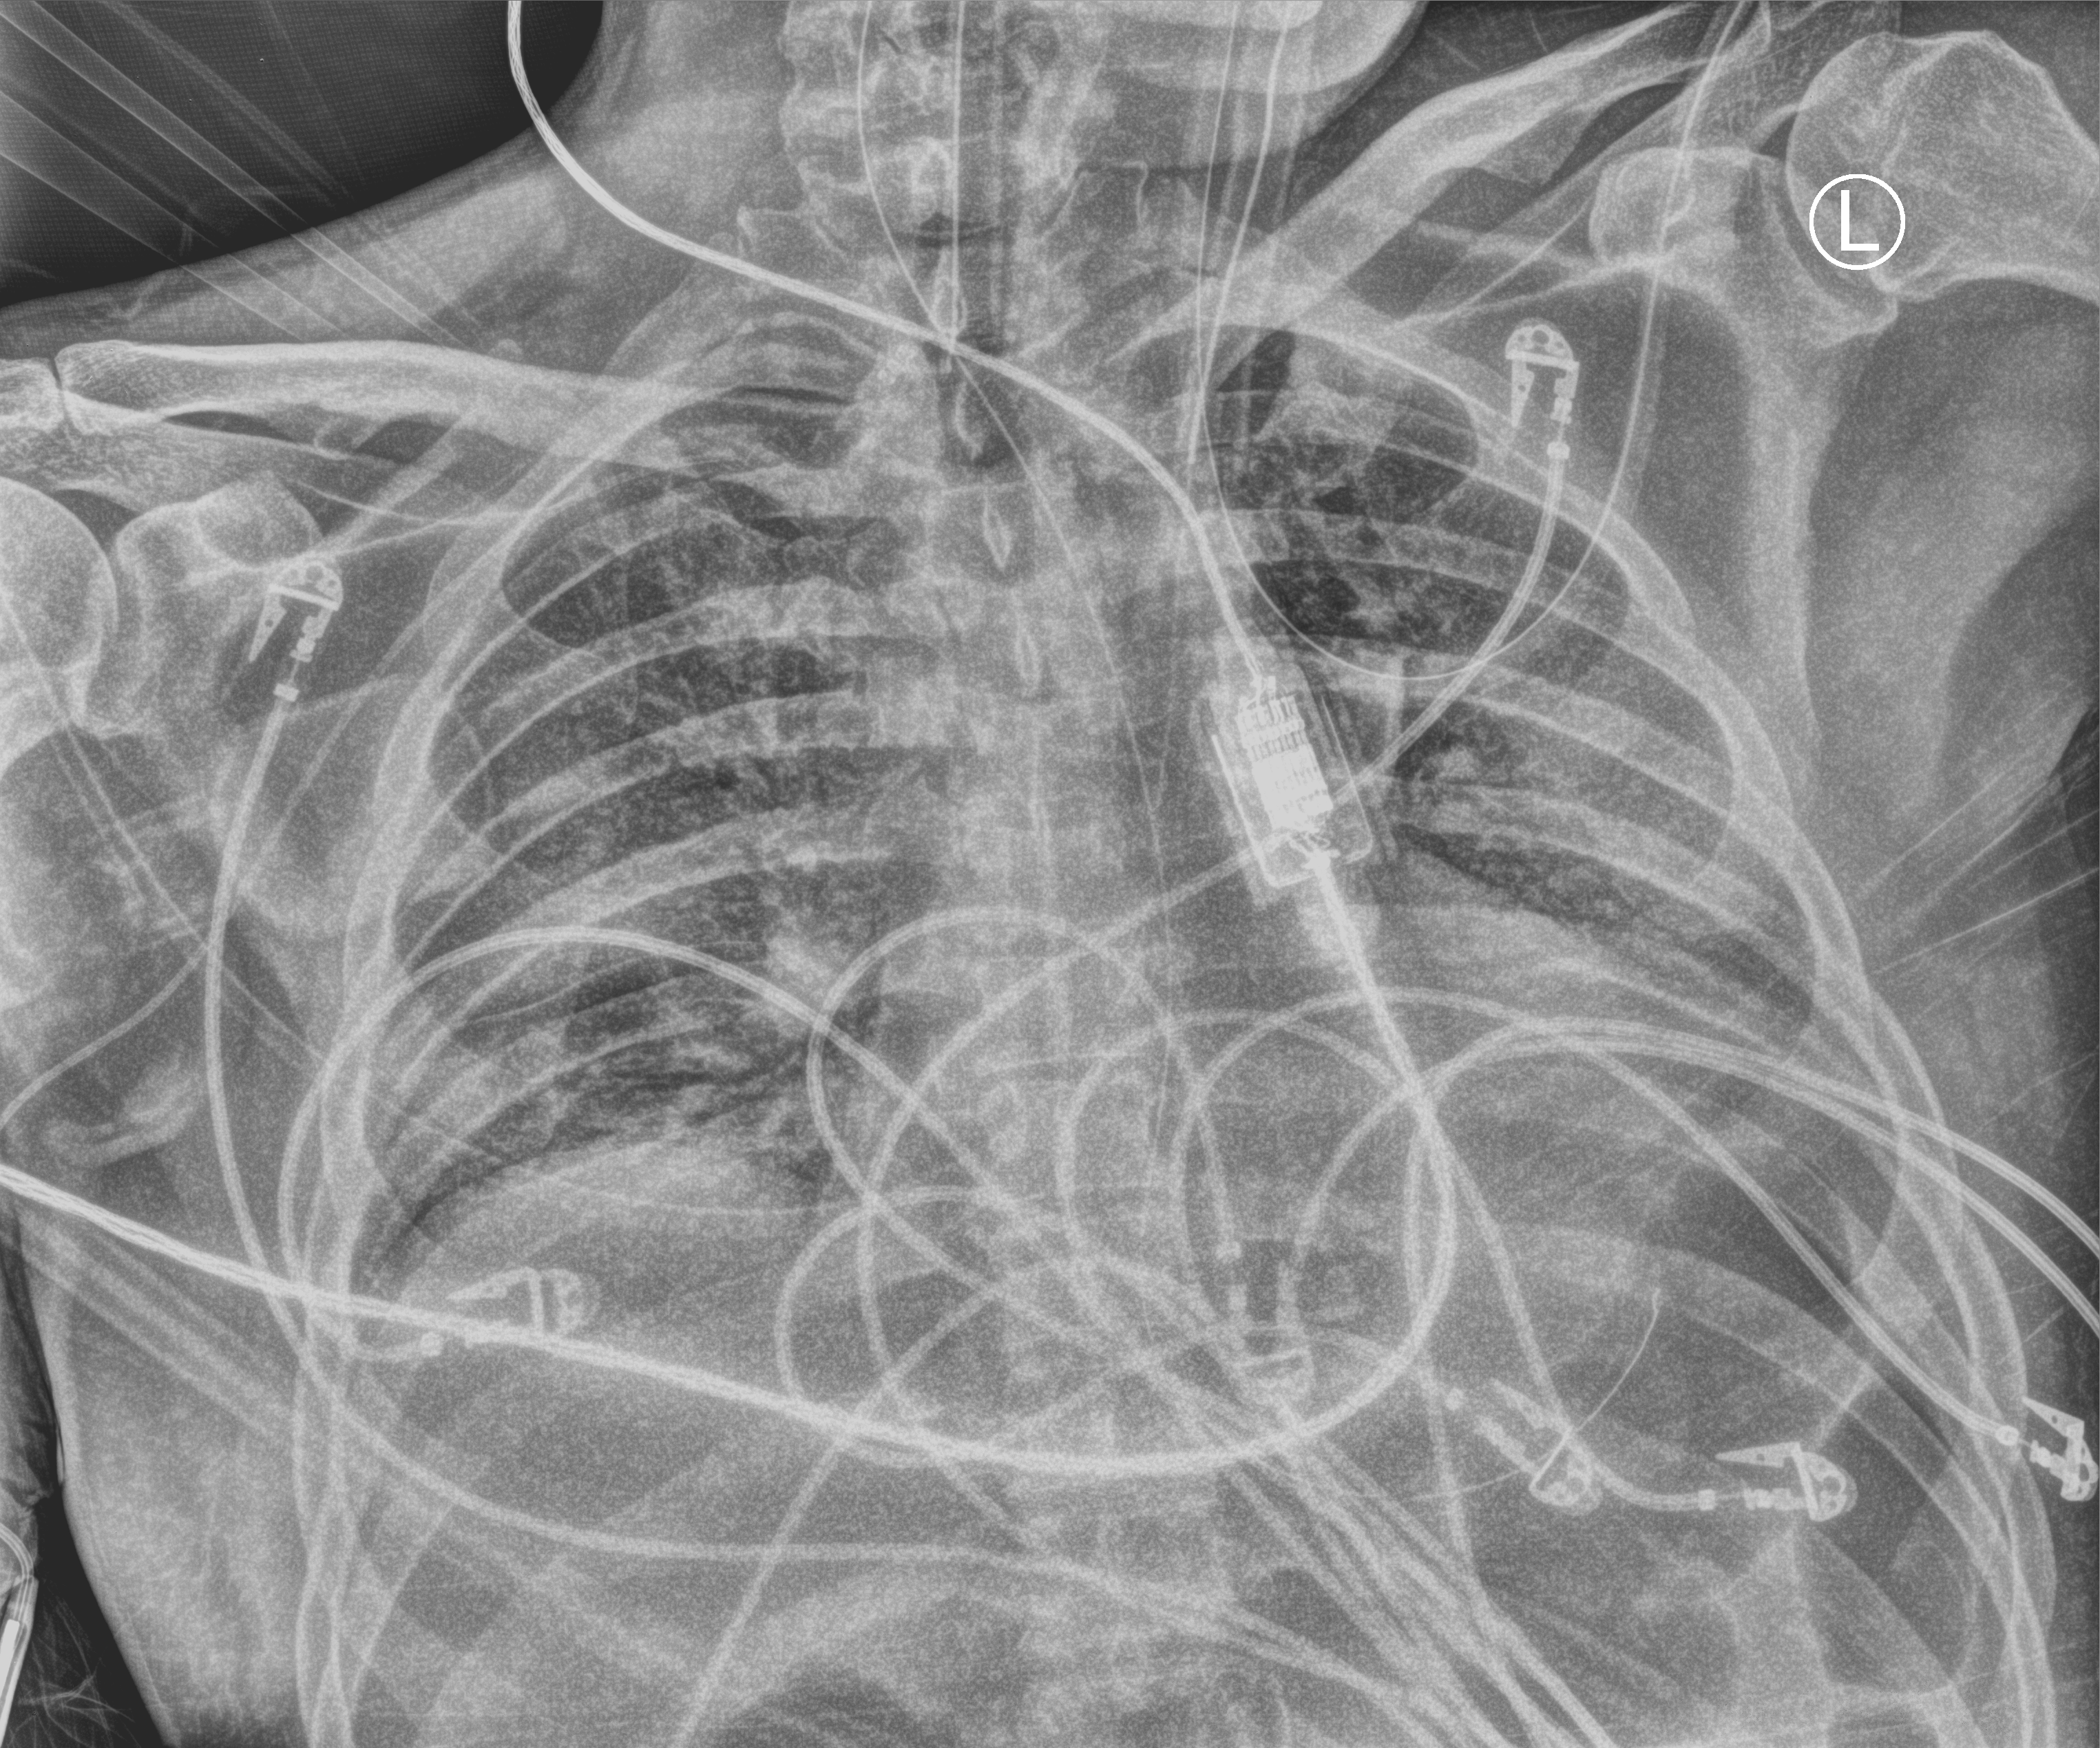
Chest X-ray (portable), anteroposterior (AP) projection. Male patient hospitalised with COVID-19, age 60–74 years.
From the hospital-stay record, not from the radiograph (when in the stay this image was taken is not recorded): admitted to intensive care during this hospital stay: yes; mechanically ventilated during this hospital stay: yes.